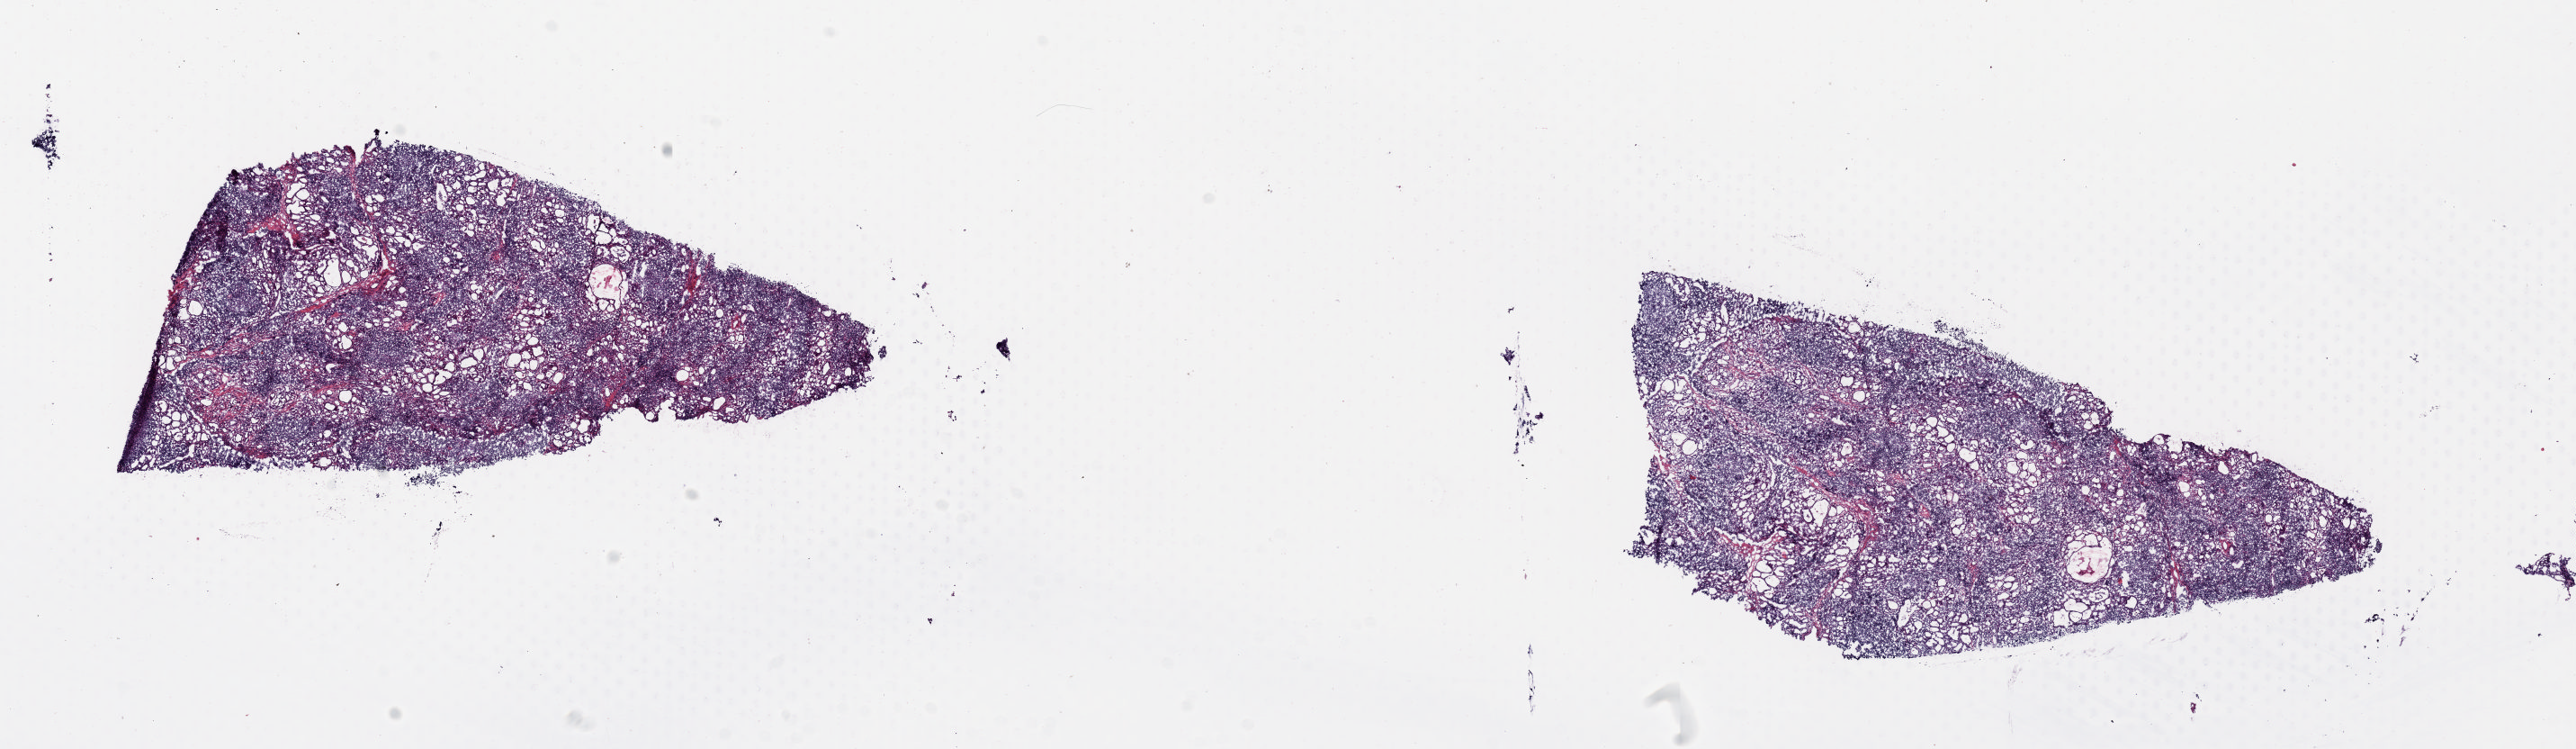
Digitized H&E-stained tissue section (whole slide) — low-resolution overview of the scanned area, about 22.6 x 6.6 mm (from a 20x scan). Frozen section from the top of the tissue portion. Solid tissue normal (non-tumour tissue) sample from the thyroid. Patient: female, age at initial diagnosis 55 years. Composition of this section per pathologist review: tumour cells 0%, tumour nuclei 0%, normal cells 100%, stromal cells 0%, necrosis 0%. Inflammatory infiltration, as recorded: lymphocyte infiltration 0%, monocyte infiltration 0%, neutrophil infiltration 0%.
This section: solid tissue normal sample (biorepository sample class). Patient diagnosis: Papillary carcinoma, follicular variant (thyroid gland).